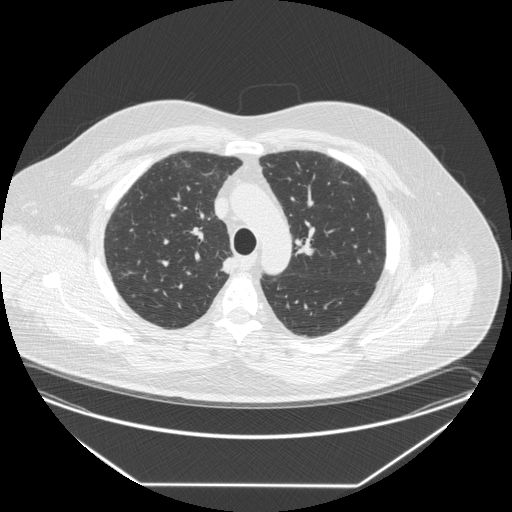
Low-dose screening chest CT, one axial slice; position 199 of 258 along the scan axis; reconstruction kernel STANDARD; 120 kVp; lung window (W 1500 / L -600 HU); 512 × 512 image matrix, field of view 440 × 440 mm.
Outlined on this slice (manually delineated by an expert):
- lesion 1 (tumor, upper lobe of right lung): bounding box (x1, y1, x2, y2) in pixels: (221, 253, 237, 274)